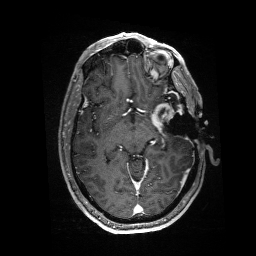
Brain MRI from a brain-tumour surgery series, one axial slice; slice 94 of 176 in the series (ordered by position); T1-weighted post-contrast; 256 × 256 image matrix, field of view 256 × 256 mm. Case-level facts recorded for this patient, not image findings: histopathology: Glioblastoma; WHO grade: 4.
Annotated regions visible in this slice (expert manual segmentation):
- residual tumour: box from (x=151, y=102) to (x=184, y=133) px